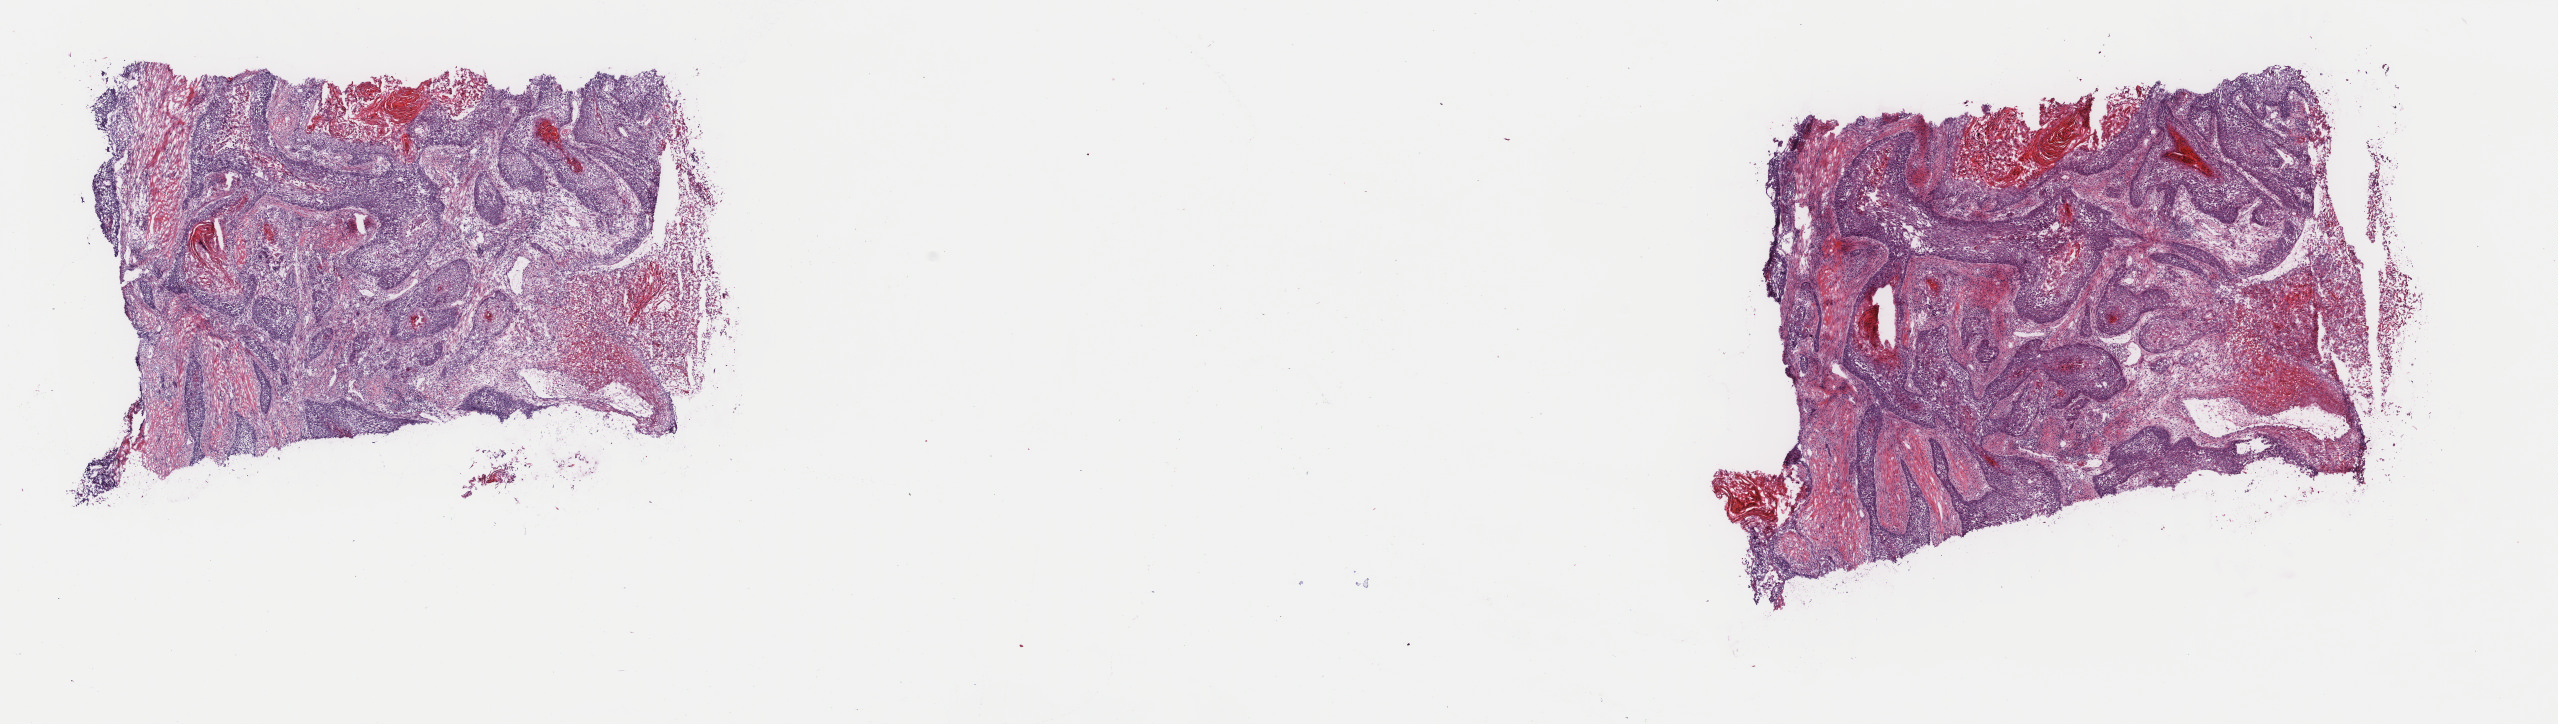
Hematoxylin and eosin (H&E) stained whole-slide image — low-resolution overview of the scanned area, about 20.3 x 5.7 mm (acquisition: 40x scan). Frozen section from the top of the tissue portion. Head and neck, primary tumour sample. Patient: female, age at initial diagnosis 61 years. Histologic grade: G2 (moderately differentiated). Slide review estimates, as recorded: tumour cells 50%, tumour nuclei 70%, normal cells 0%, stromal cells 50%, necrosis 0%. Inflammatory infiltration, as recorded: lymphocyte infiltration 10%, monocyte infiltration 0%, neutrophil infiltration 0%.
- AJCC pathologic stage: III (7th edition)
- laterality: left
- pathologic diagnosis: Squamous cell carcinoma, keratinizing, NOS (tongue, NOS)